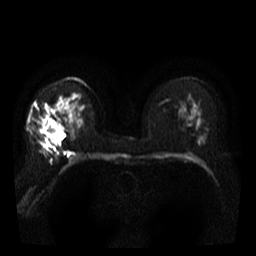
Breast MRI, one axial slice. Slice 22 of 40 in the series (ordered by position). Diffusion-weighted series; image 2 of 4 stored at this slice position (different b-values; order by instance number). 3 T. 5 mm slice thickness. 256 × 256 image matrix. Female patient.
Outlined on this slice (manually delineated by an expert):
- tumour on diffusion-weighted imaging: bounding box (x1, y1, x2, y2) in pixels: (39, 127, 63, 148)